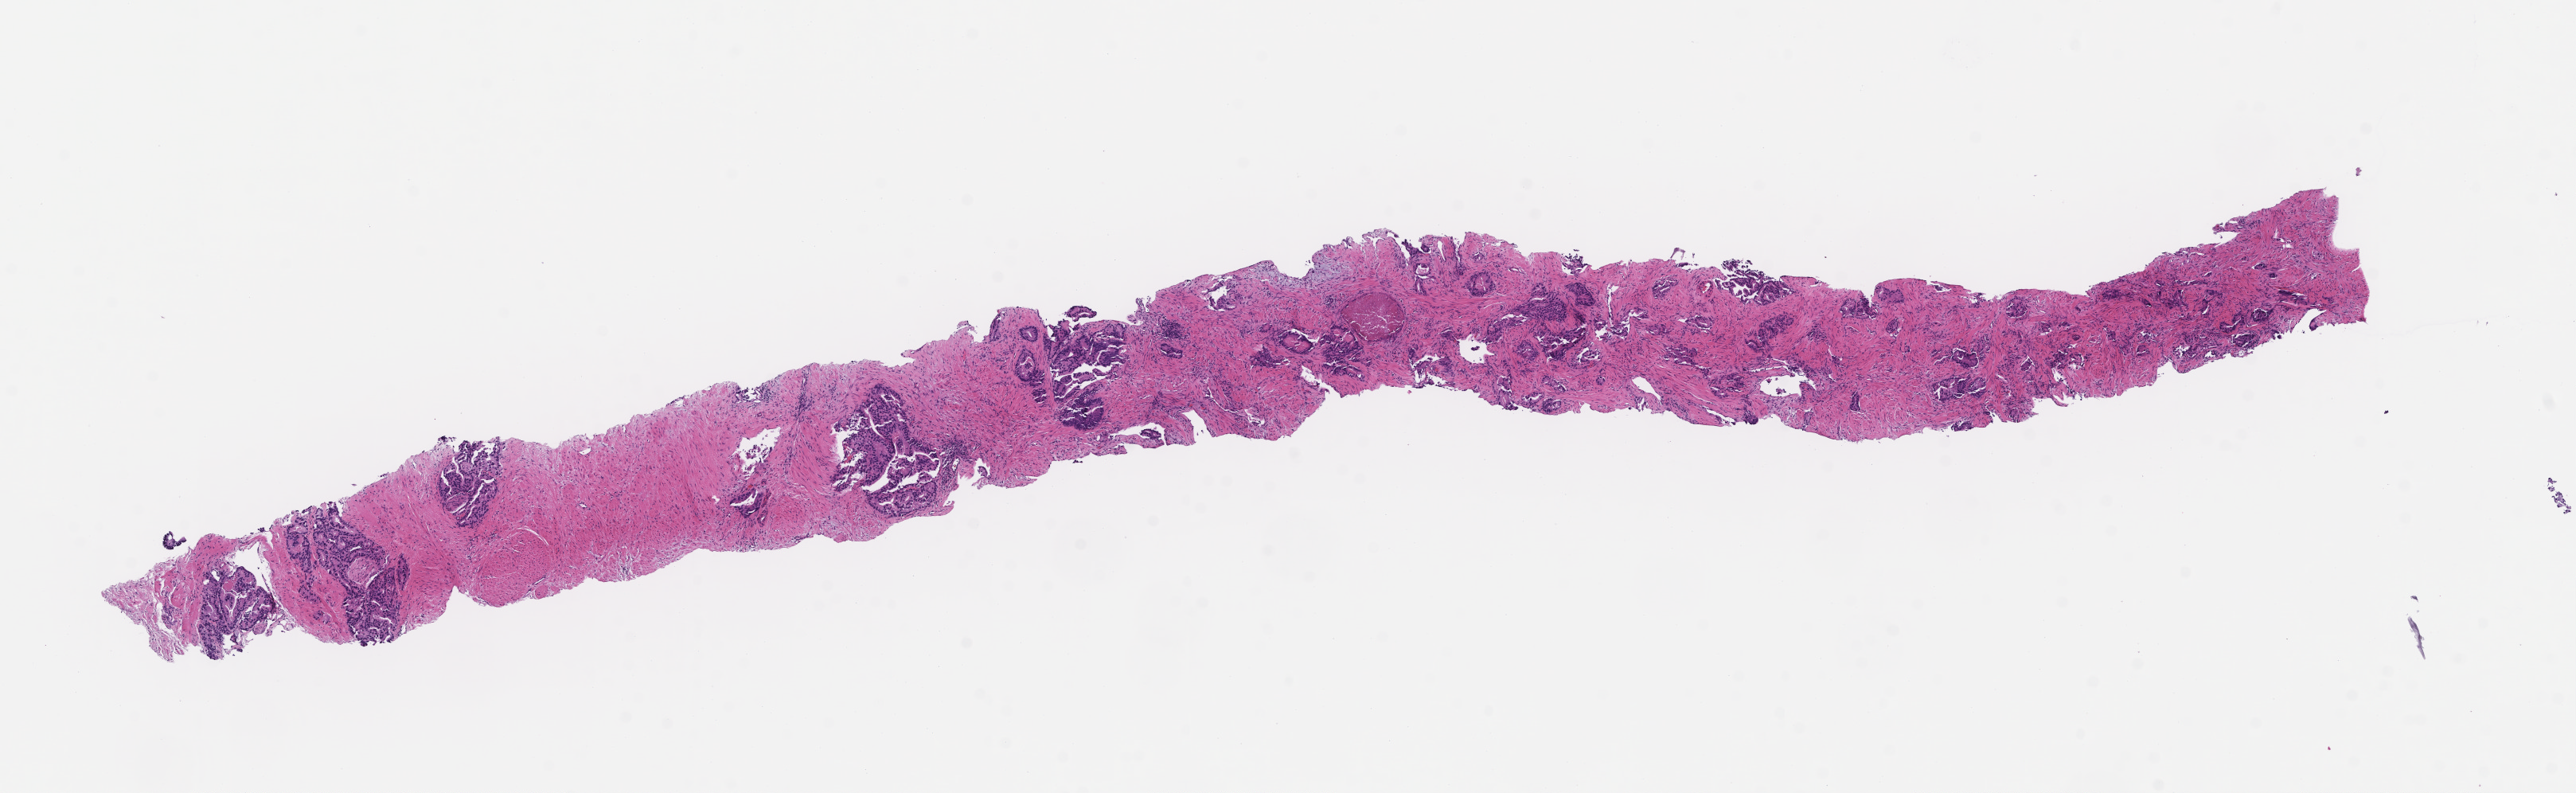
Whole-slide image, H&E stain, low-resolution overview of the scanned area, about 13.1 x 4.0 mm; formalin-fixed, paraffin-embedded (FFPE) tissue; archival tissue. Patient sex: male.
This section: metastatic tumor tissue. Patient diagnosis (primary): Prostate Carcinoma.